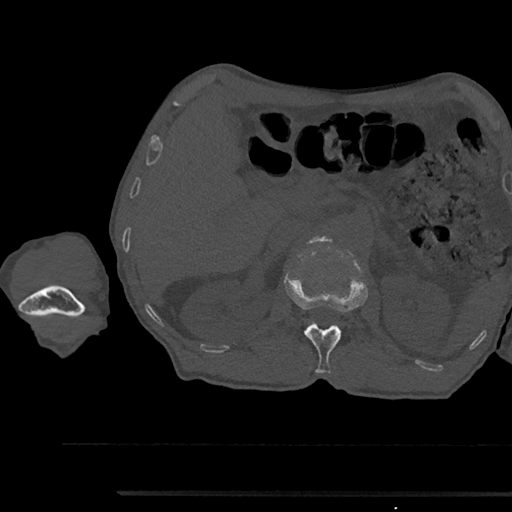
CT including the spine, one axial slice; slice 623 of 797 in the series (ordered by position); 120 kVp; bone window (W 1800 / L 400 HU); 0.5 mm slice thickness; 512 × 512 image matrix, field of view 367 × 367 mm. Male patient, age 79 years. Case-level facts recorded for this patient, not image findings: primary cancer: prostate.
Annotated regions visible in this slice (semi-automatic segmentation, software-assisted and operator-edited):
- L1 vertebra: bounding box [x1, y1, x2, y2] px = [285, 277, 367, 374]
- L2 vertebra: [308, 236, 332, 244]